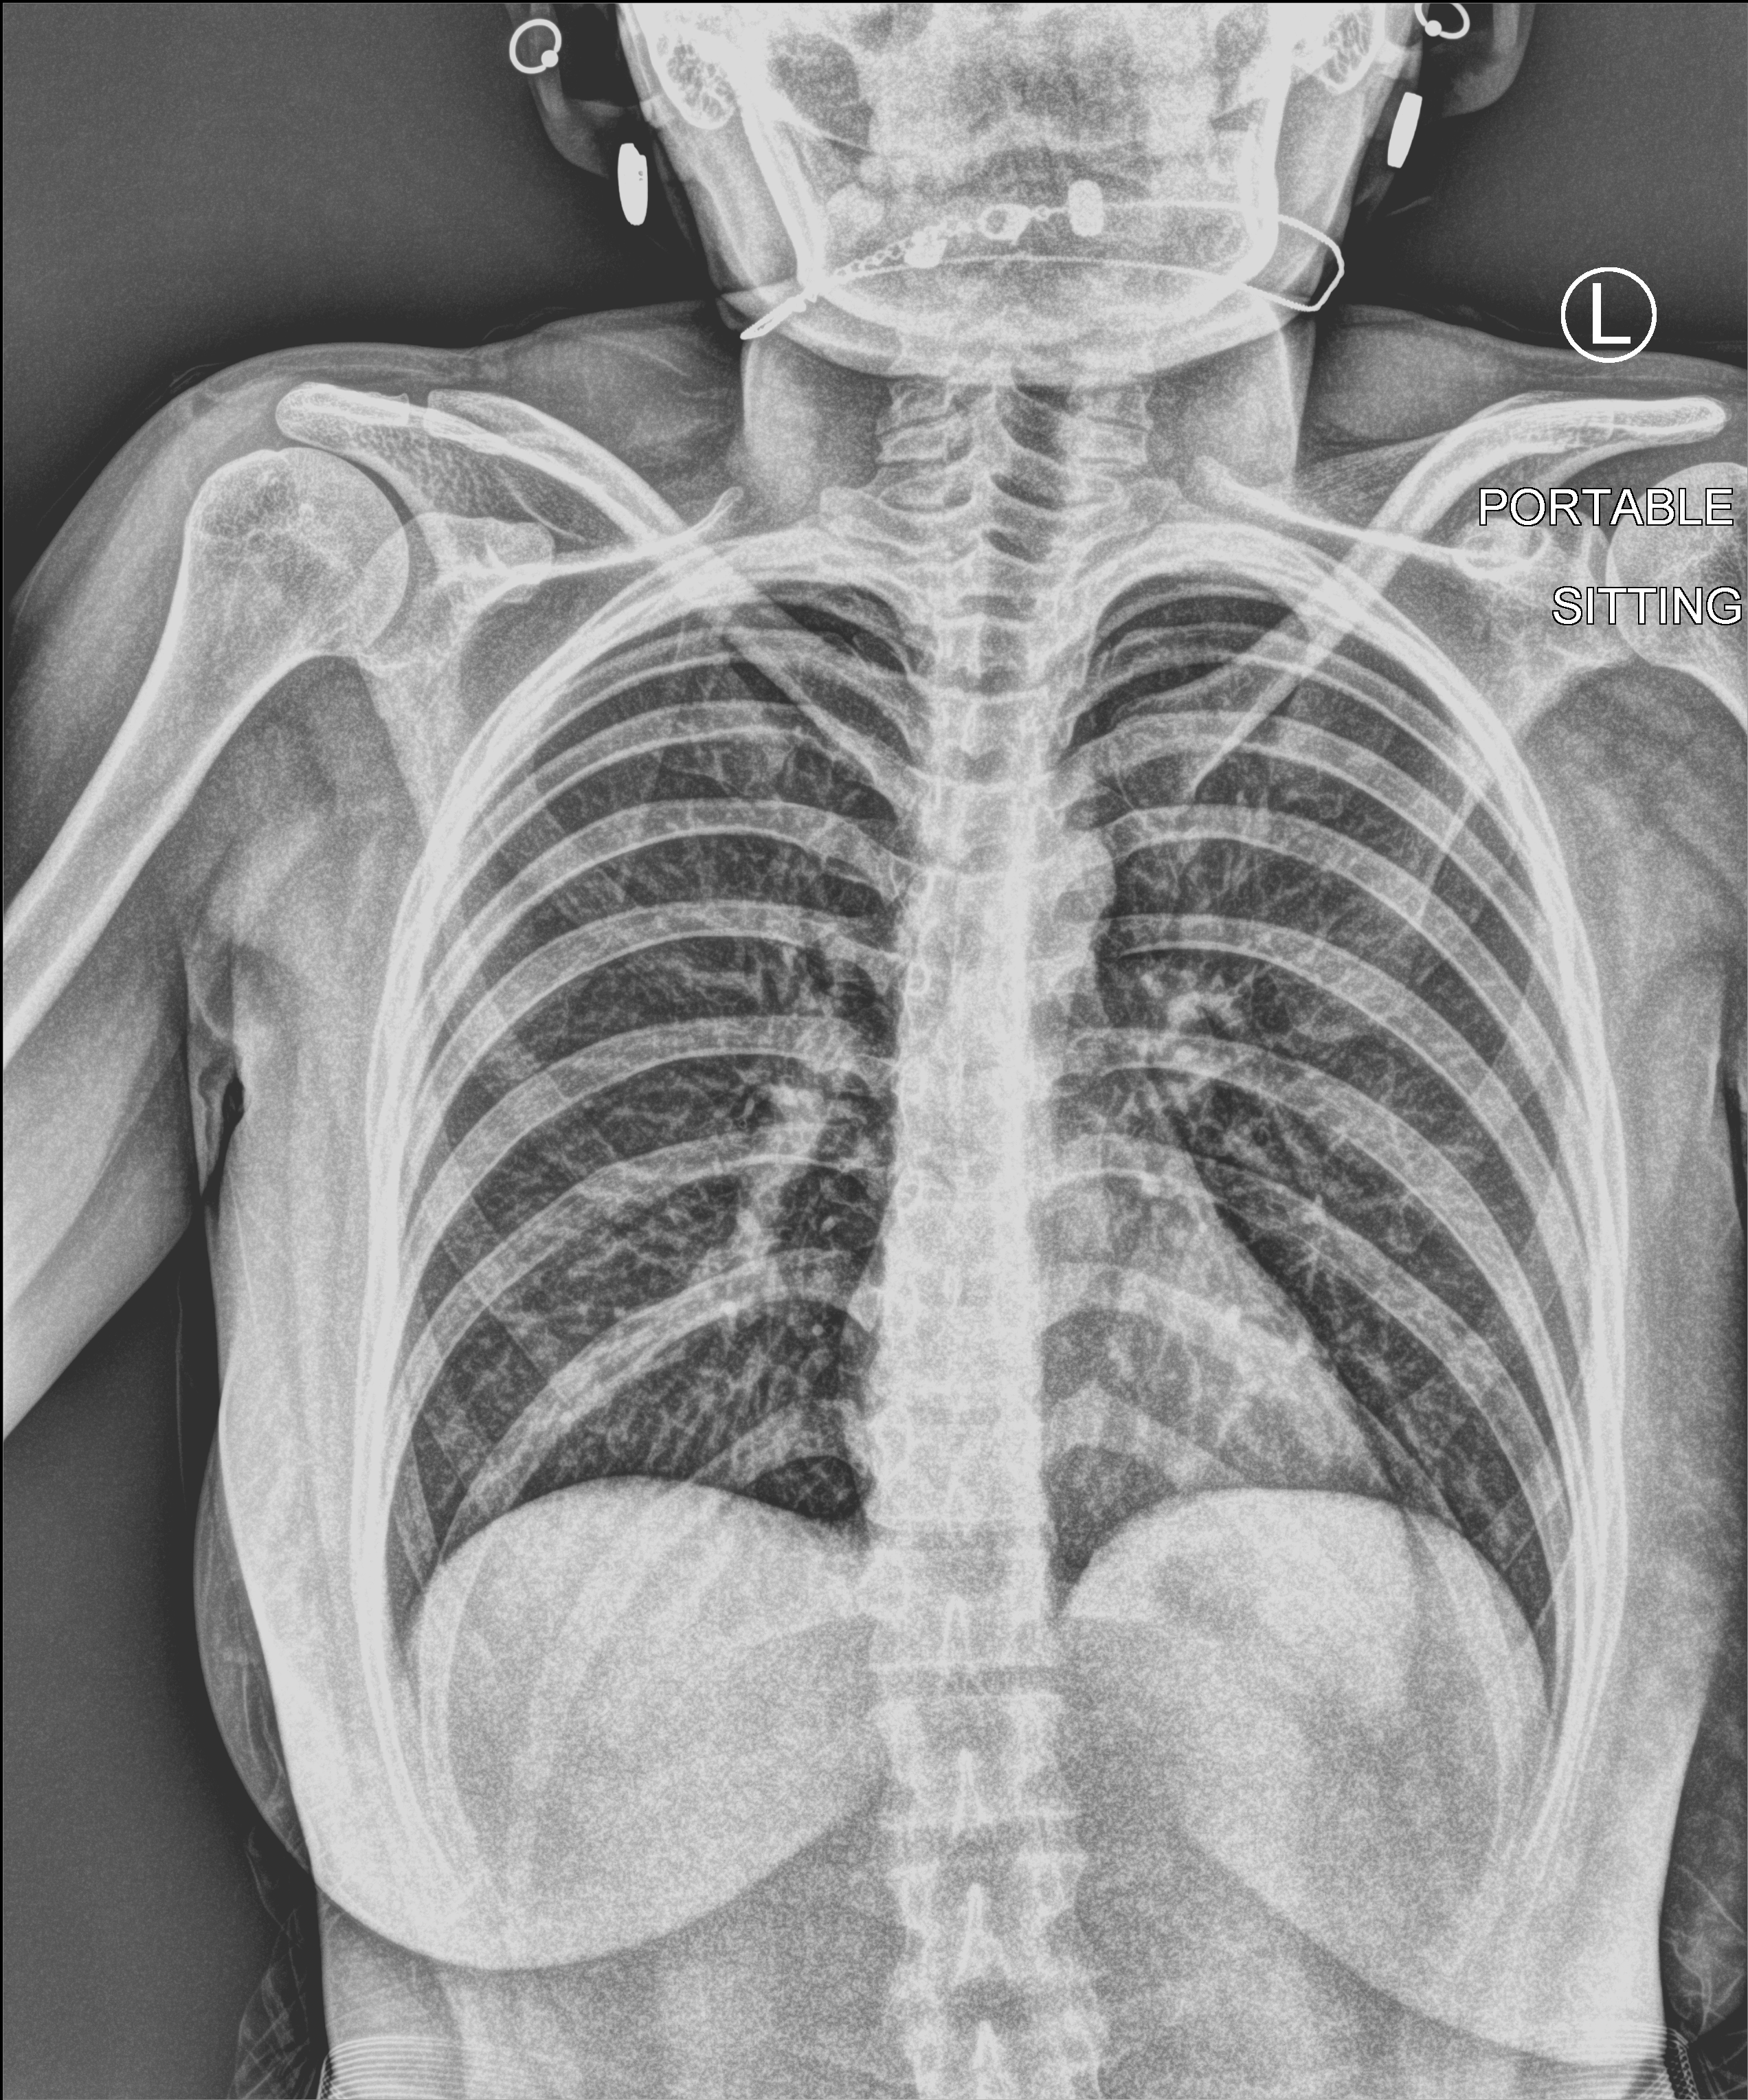
Bedside chest radiograph (computed radiography), anteroposterior (AP) projection. Patient hospitalised with COVID-19; female, aged 18–59 years.
From the hospital-stay record, not from the radiograph (when in the stay this image was taken is not recorded): mechanically ventilated during this hospital stay: no.